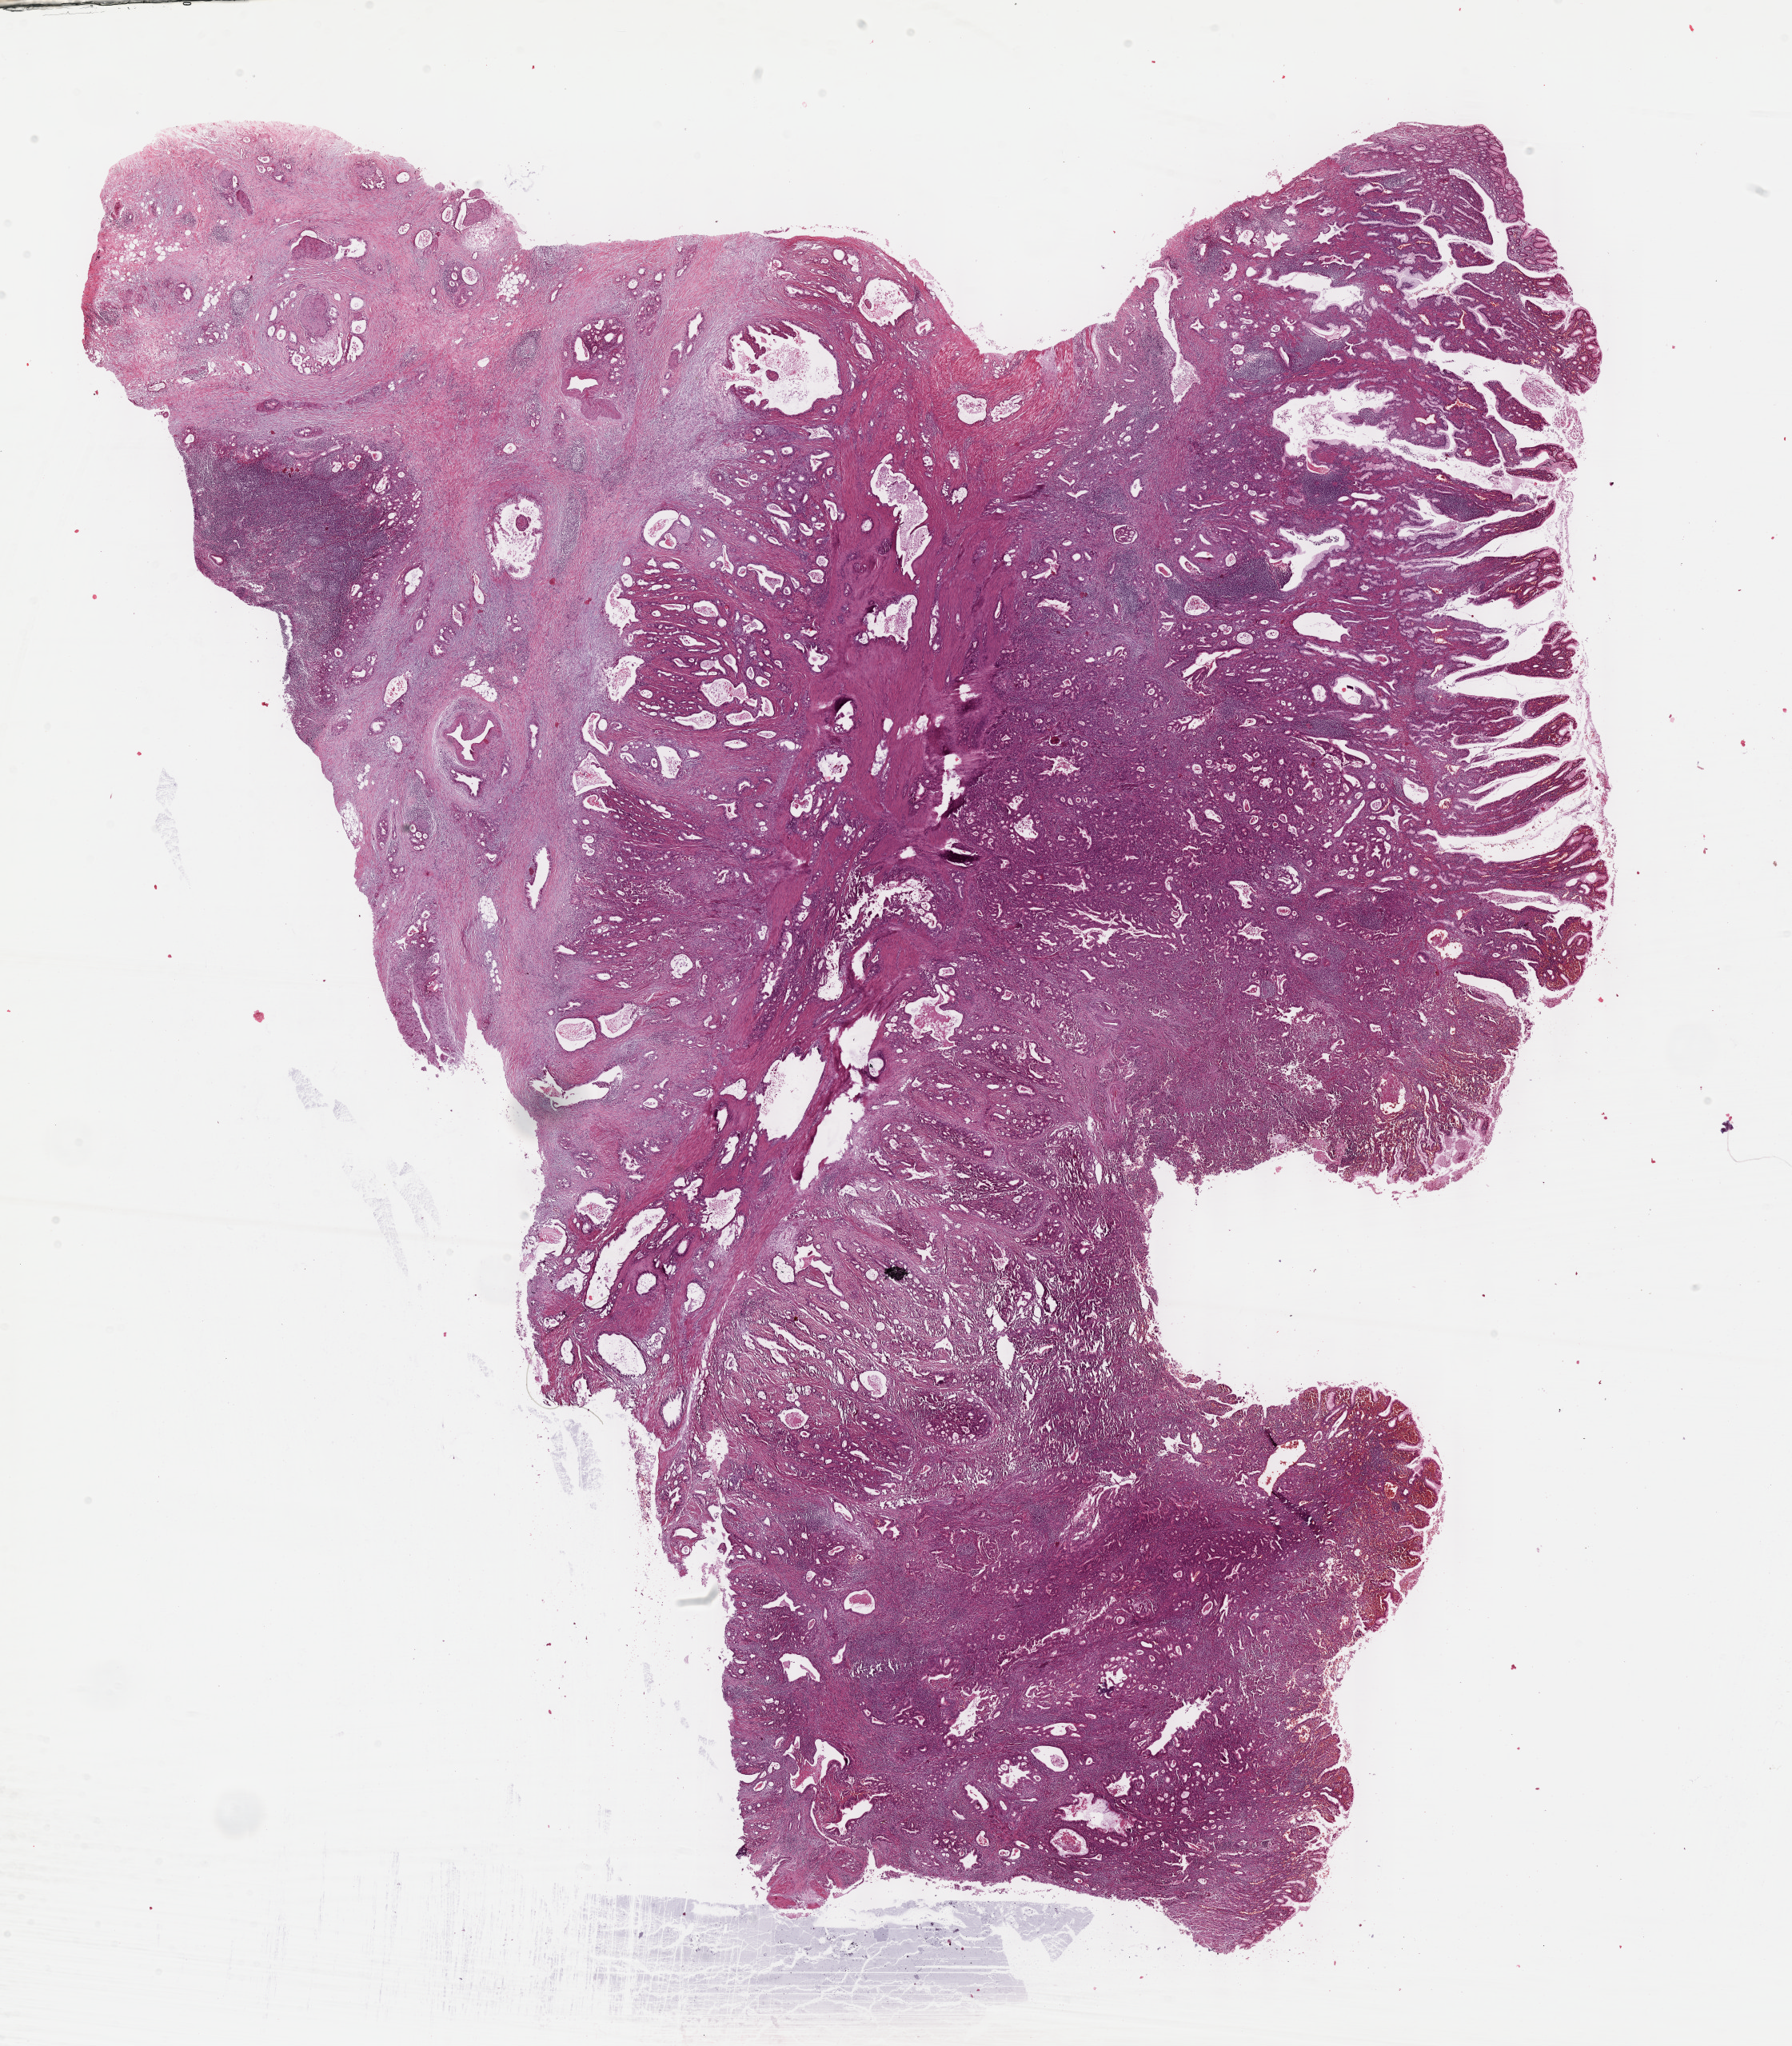
Whole-slide histology image, H&E, whole scanned area (about 18.1 x 20.7 mm) shown as a low-resolution overview. Formalin-fixed paraffin-embedded (FFPE) diagnostic section. Sample: primary tumour, stomach. Male, age 52 years at initial diagnosis. Histologic grade: G2 (moderately differentiated).
TNM: T3 N0 M0. Diagnosis: Adenocarcinoma, NOS (cardia, NOS). AJCC pathologic stage: II.